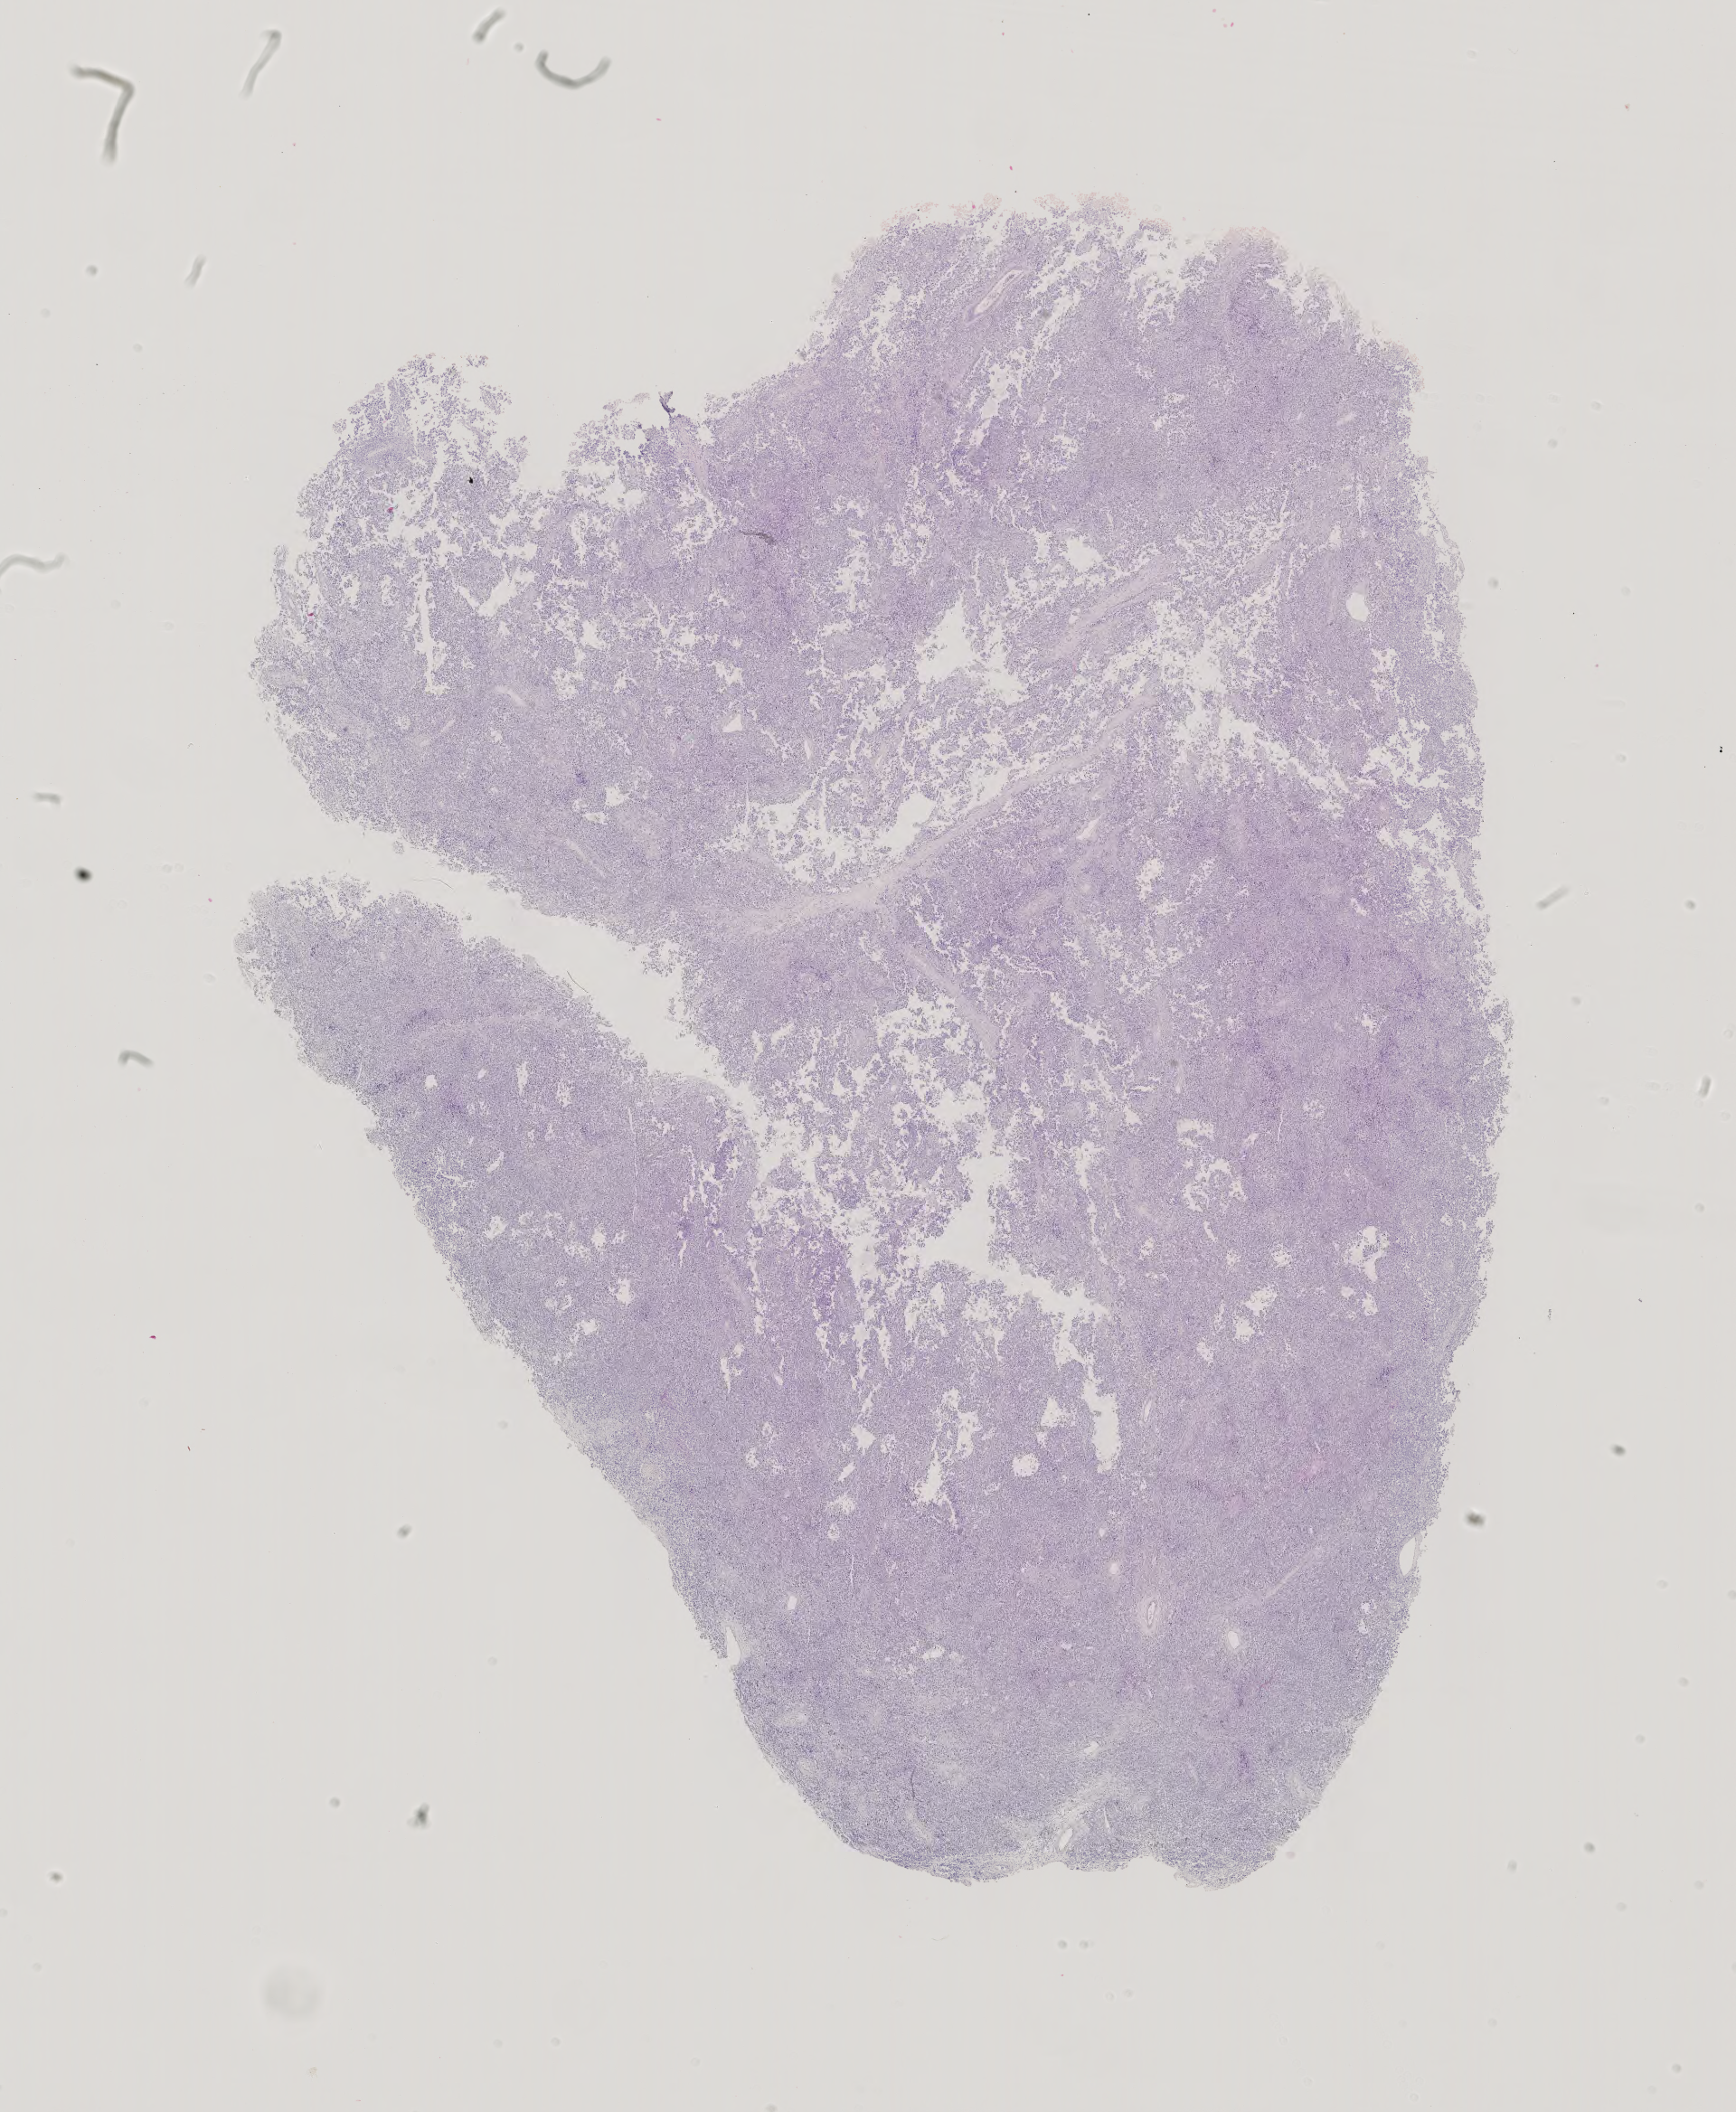
Whole-slide histology image, H&E-stained, shown as a low-resolution overview of the whole scanned area (about 14.0 x 17.0 mm, acquisition: 40x scan), formalin-fixed paraffin-embedded (FFPE) diagnostic section, sample: primary tumour, testis. Male patient; age at initial diagnosis 26 years.
Diagnosis: Seminoma, NOS. AJCC pathologic stage: I (4th edition).